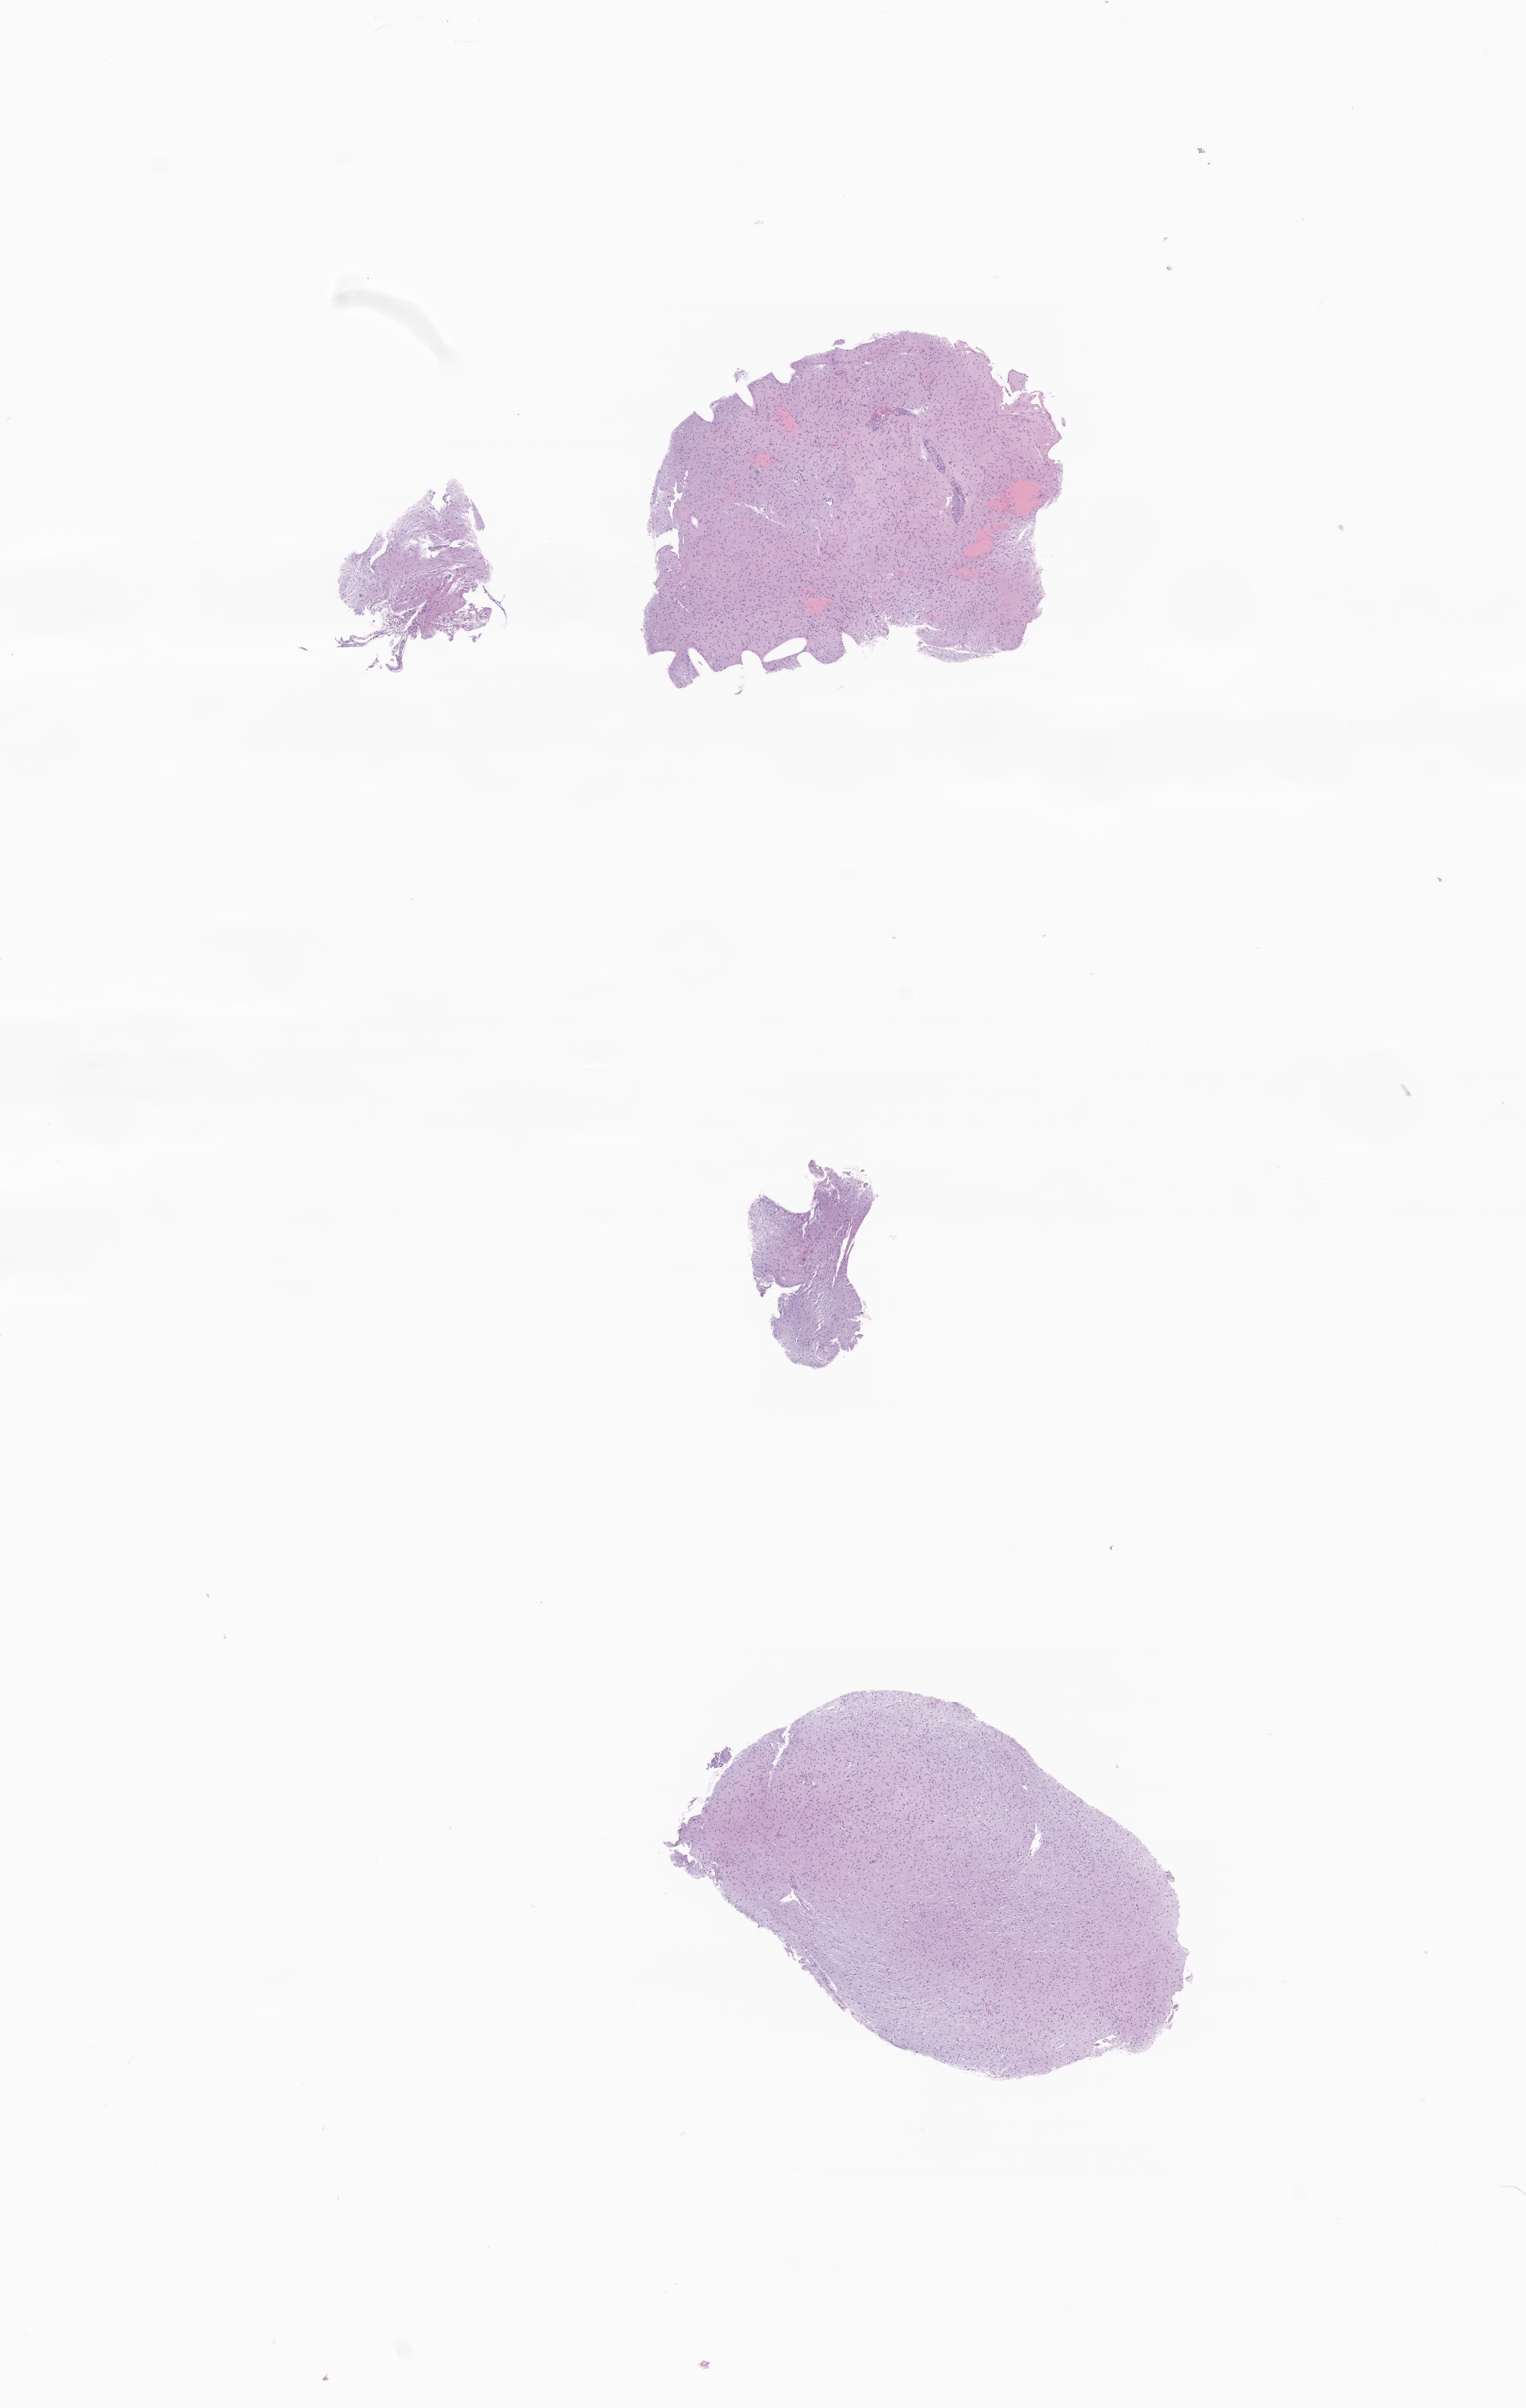
Haematoxylin and eosin whole-slide image of tumor tissue from the brain stem — whole scanned area (about 8.5 x 13.4 mm) shown as a low-resolution overview. FFPE section. Patient female; age 33 months (2 years 9 months).
Recorded diagnosis: Pilocytic astrocytoma.